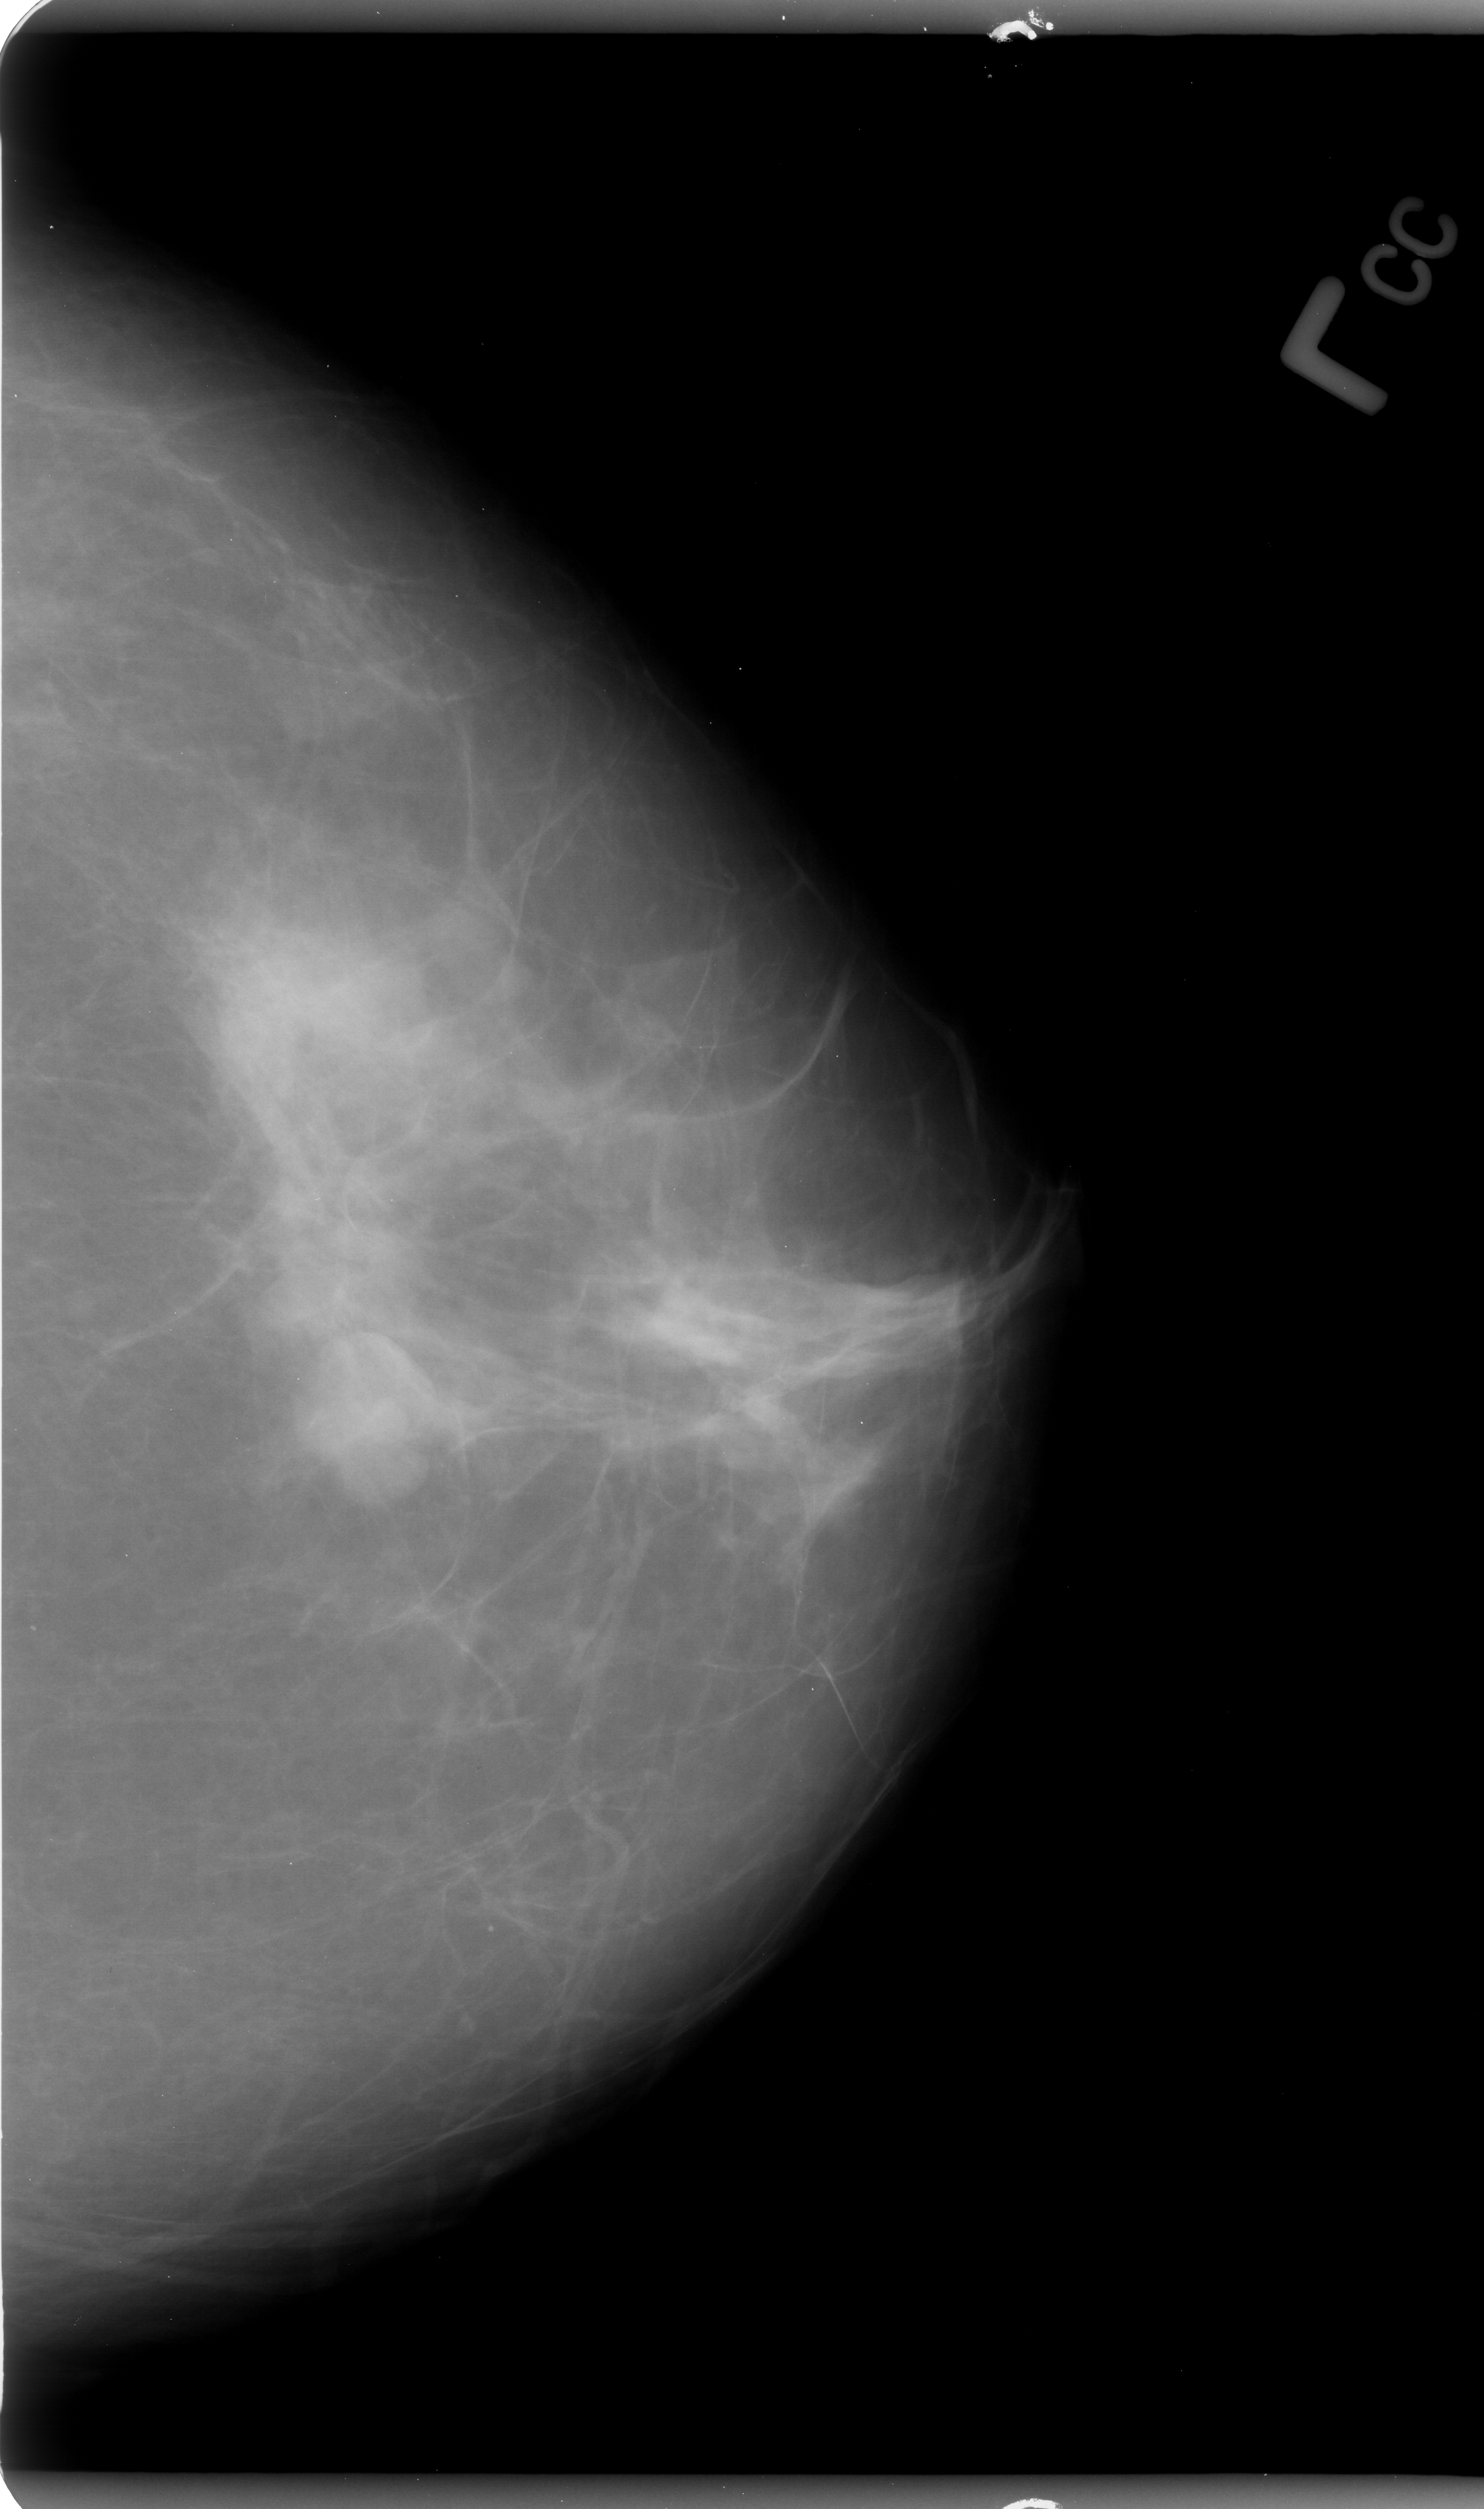
Mammogram (digitized film); left breast; CC view; BI-RADS breast density category 2 (scale 1–4).
Marked findings (only marked abnormalities are described; nothing is implied about the rest of the image): mass, shape lobulated, margins circumscribed; BI-RADS assessment category 4; pathology result (as recorded, not read from the image): benign.